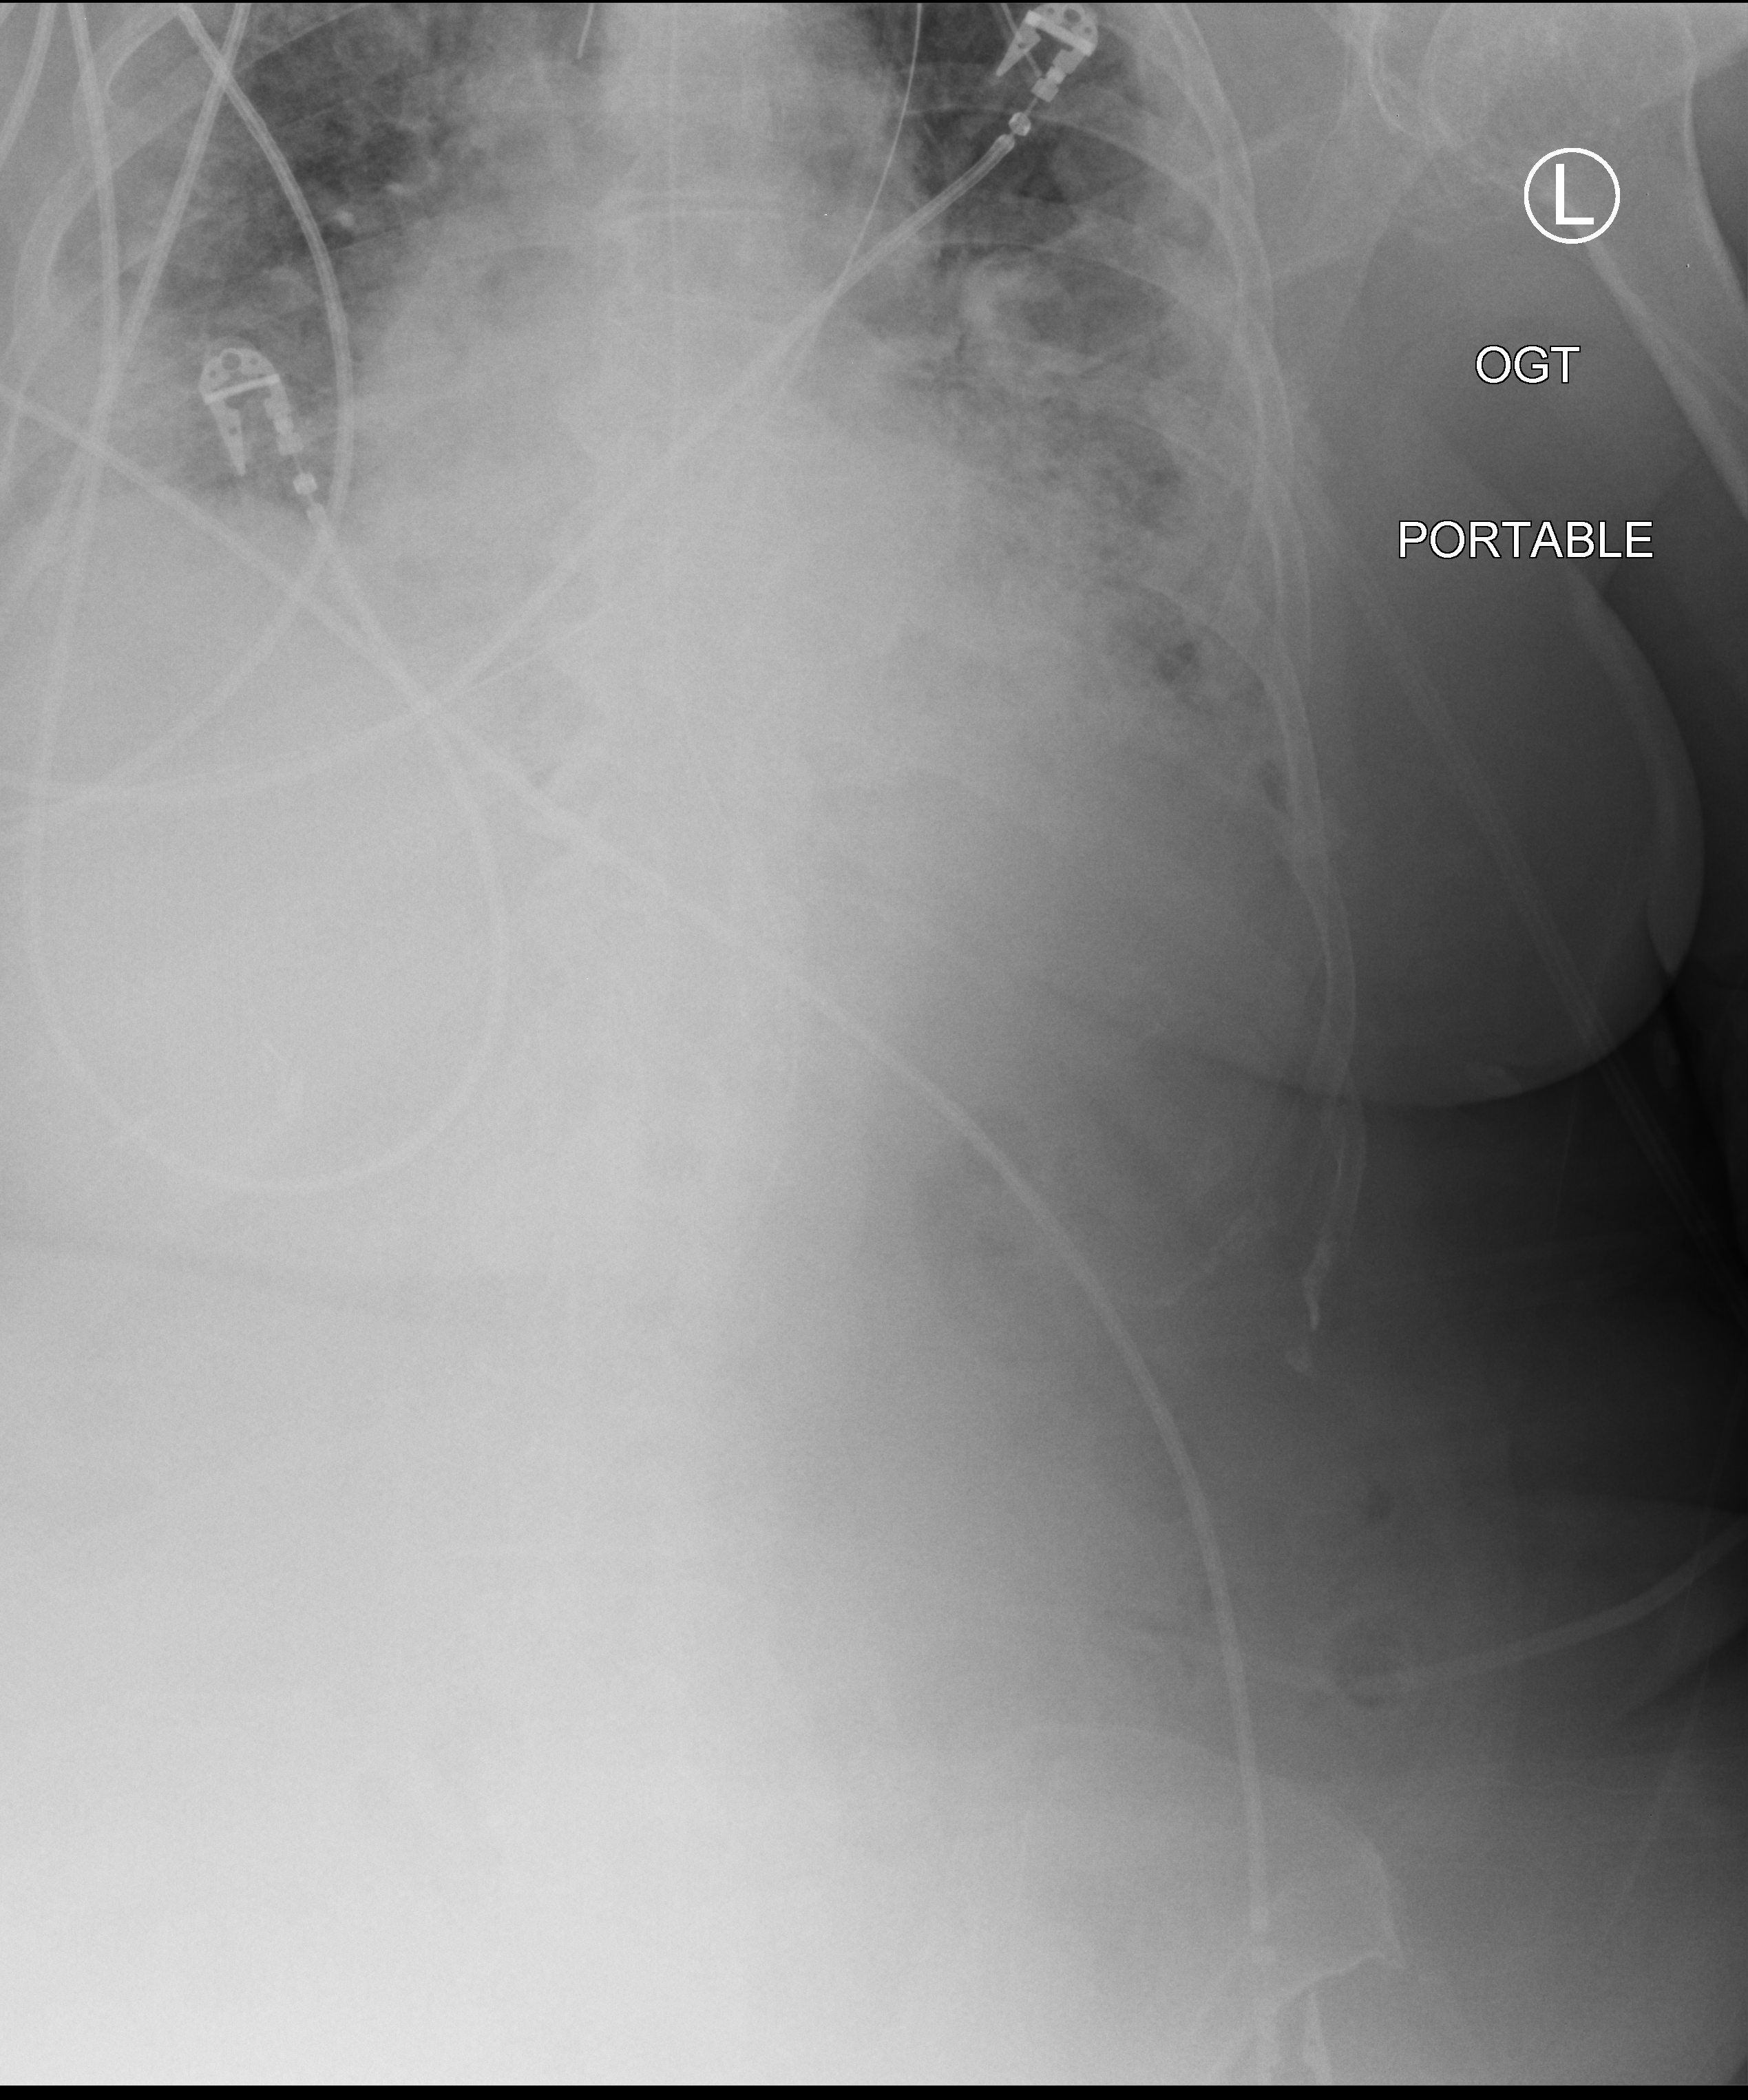
Portable chest radiograph, anteroposterior (AP) projection. Patient hospitalised with COVID-19; female, aged 75–90 years.
From the hospital-stay record, not from the radiograph (when in the stay this image was taken is not recorded):
- admitted to intensive care during this hospital stay: no
- mechanically ventilated during this hospital stay: yes